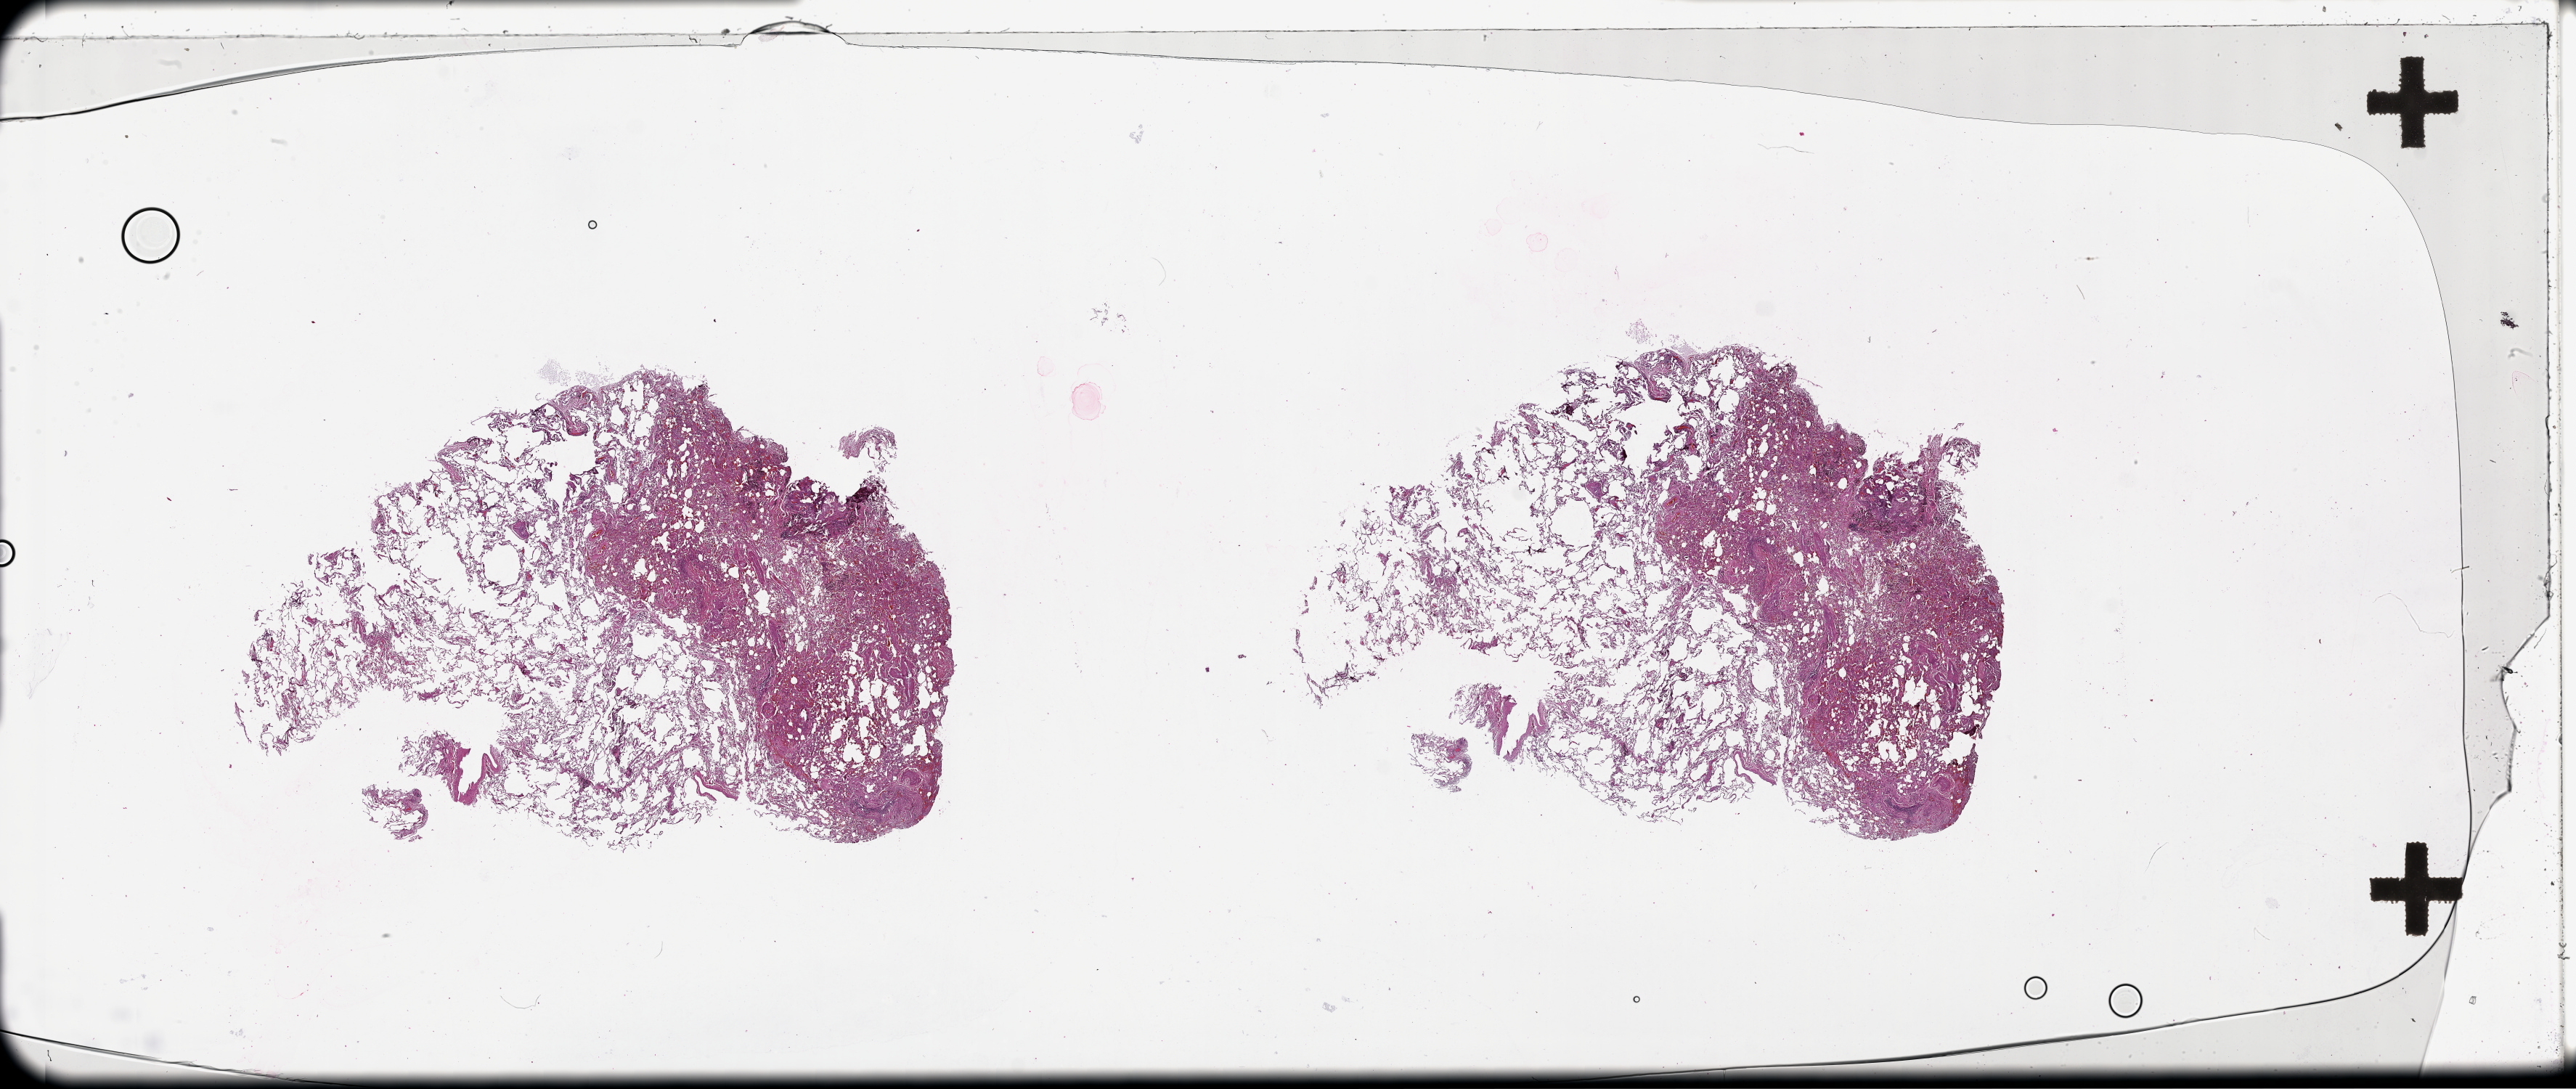
H&E-stained whole-slide image — shown as a low-resolution overview of the whole scanned area (about 57.1 x 24.2 mm, from a 20x scan), lung, normal (non-tumour) tissue. Patient: male, age 71 years.
• this section: normal (non-tumour) tissue from the same patient
• patient diagnosis (cohort enrolment): squamous cell carcinoma (lung)